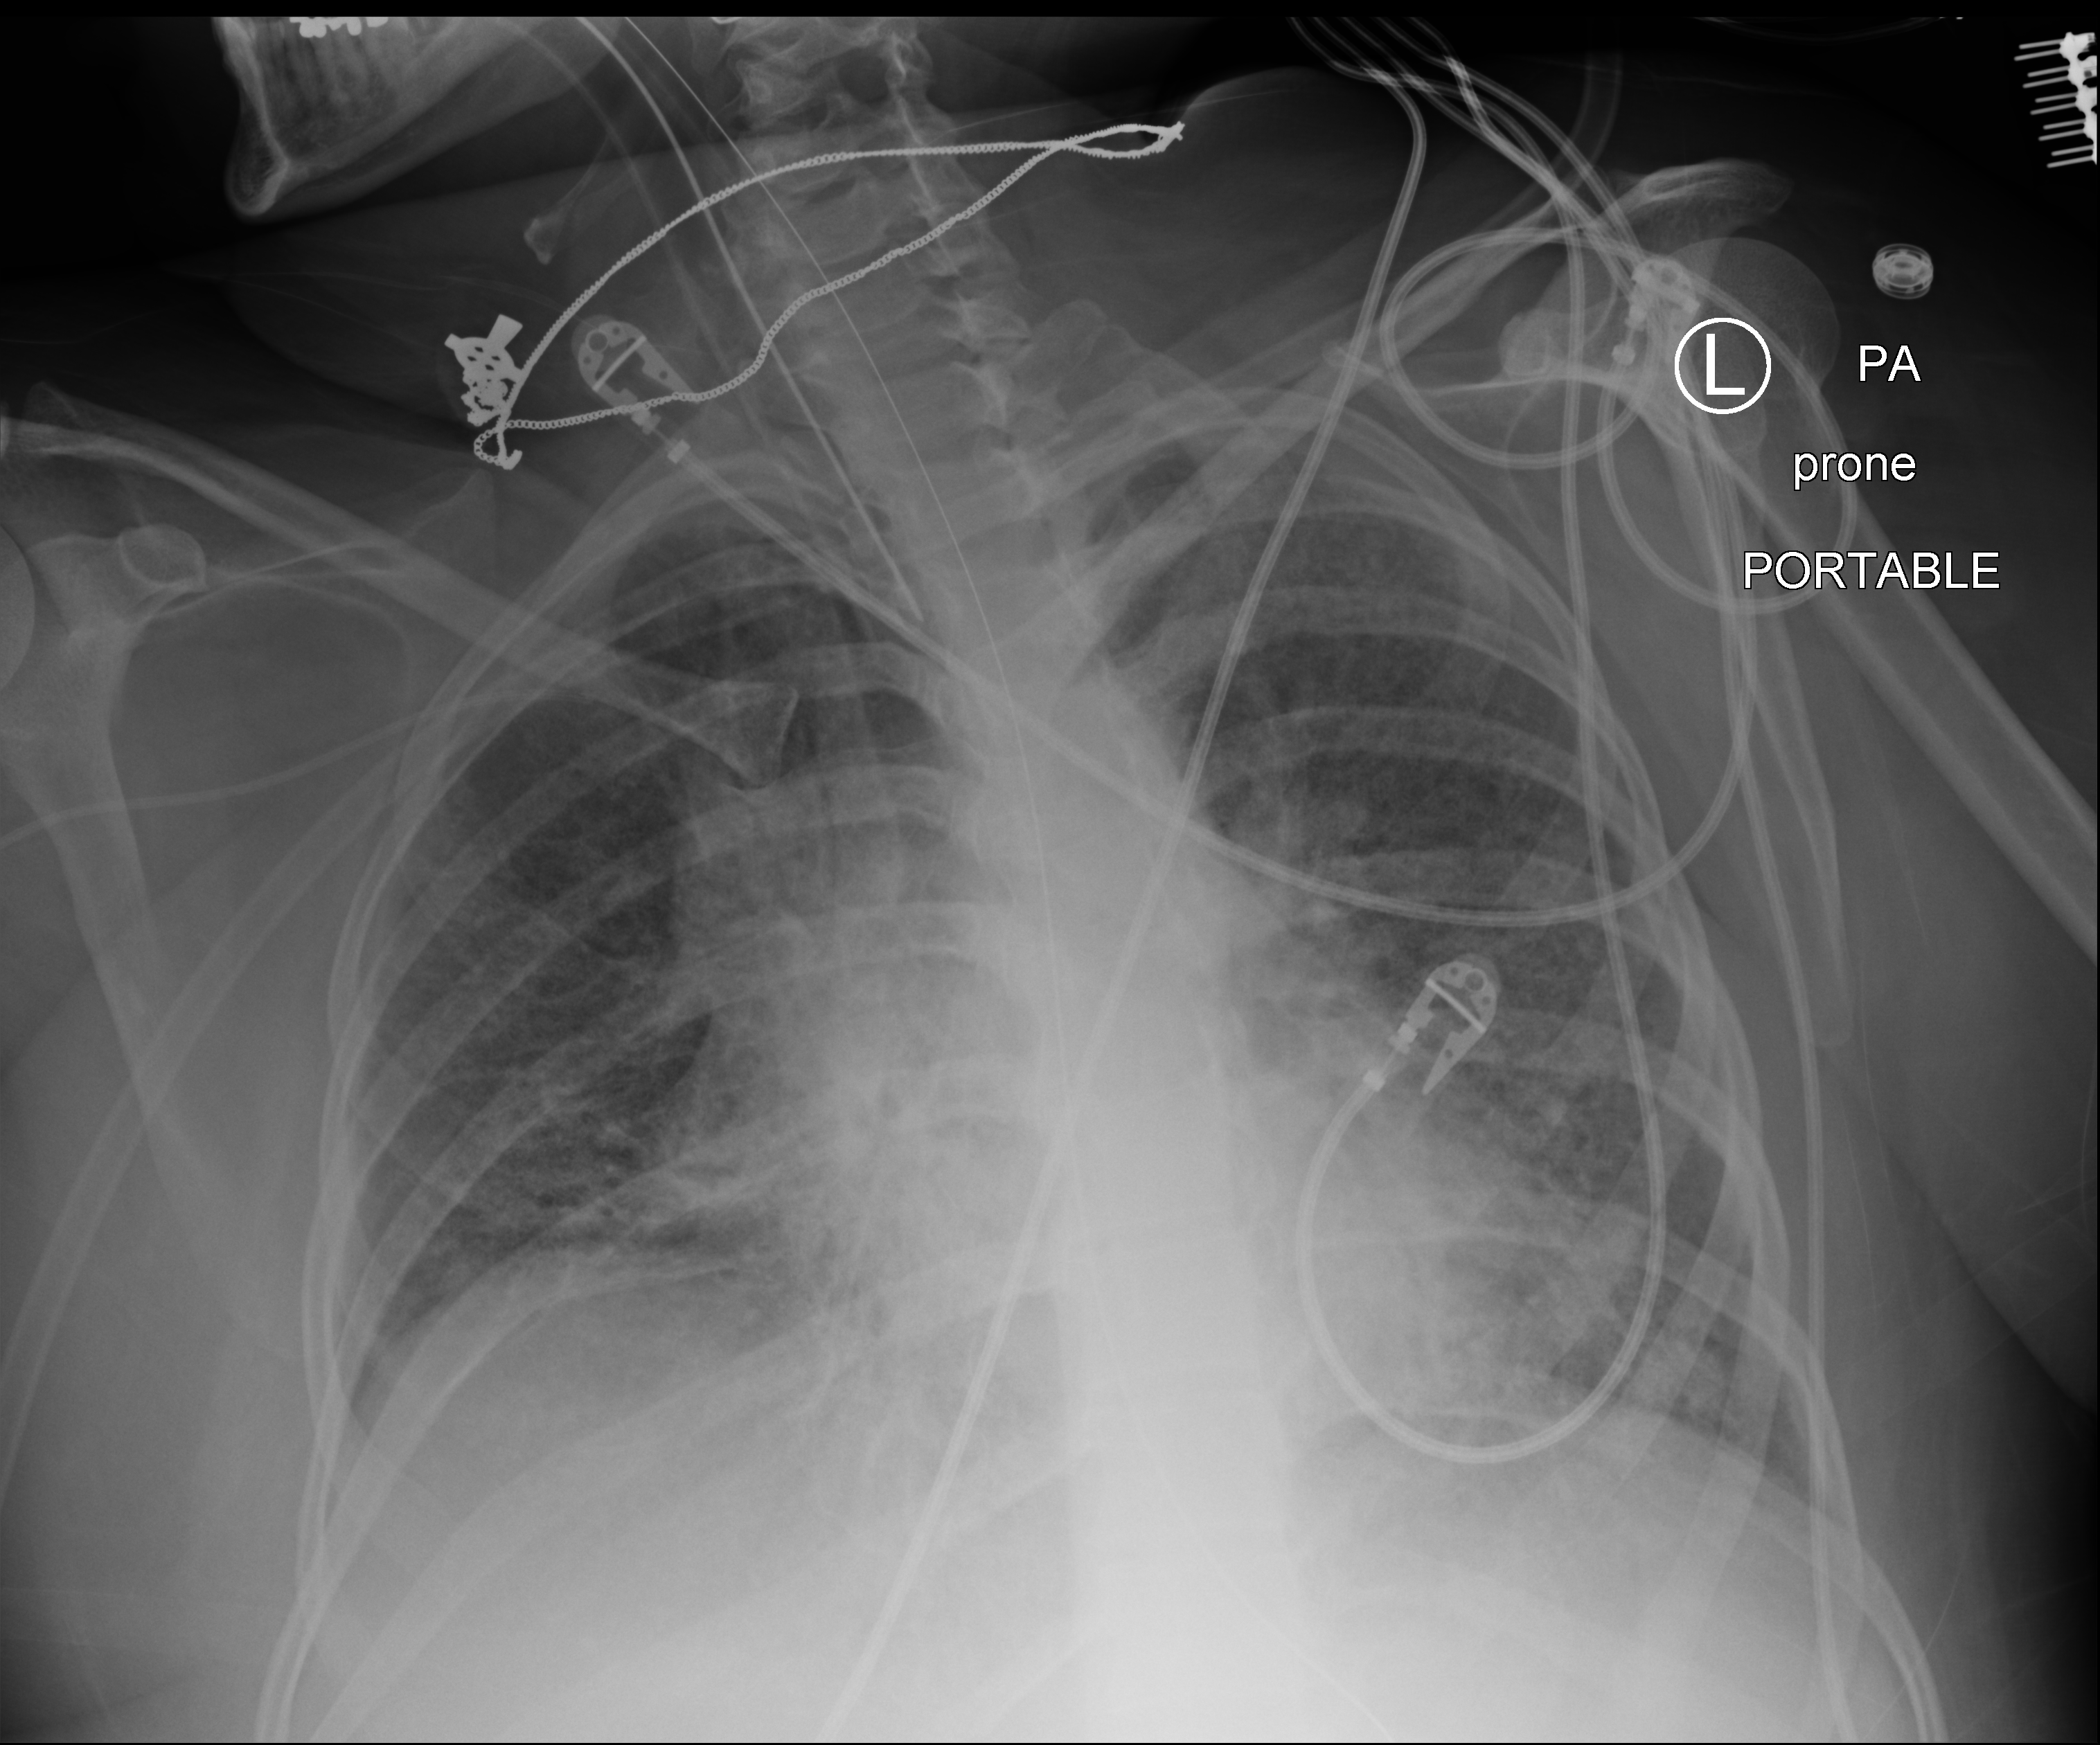
Bedside chest radiograph (computed radiography), posteroanterior (PA) projection. Female patient hospitalised with COVID-19, age 18–59 years.
From the hospital-stay record, not from the radiograph (when in the stay this image was taken is not recorded):
- mechanically ventilated during this hospital stay: yes